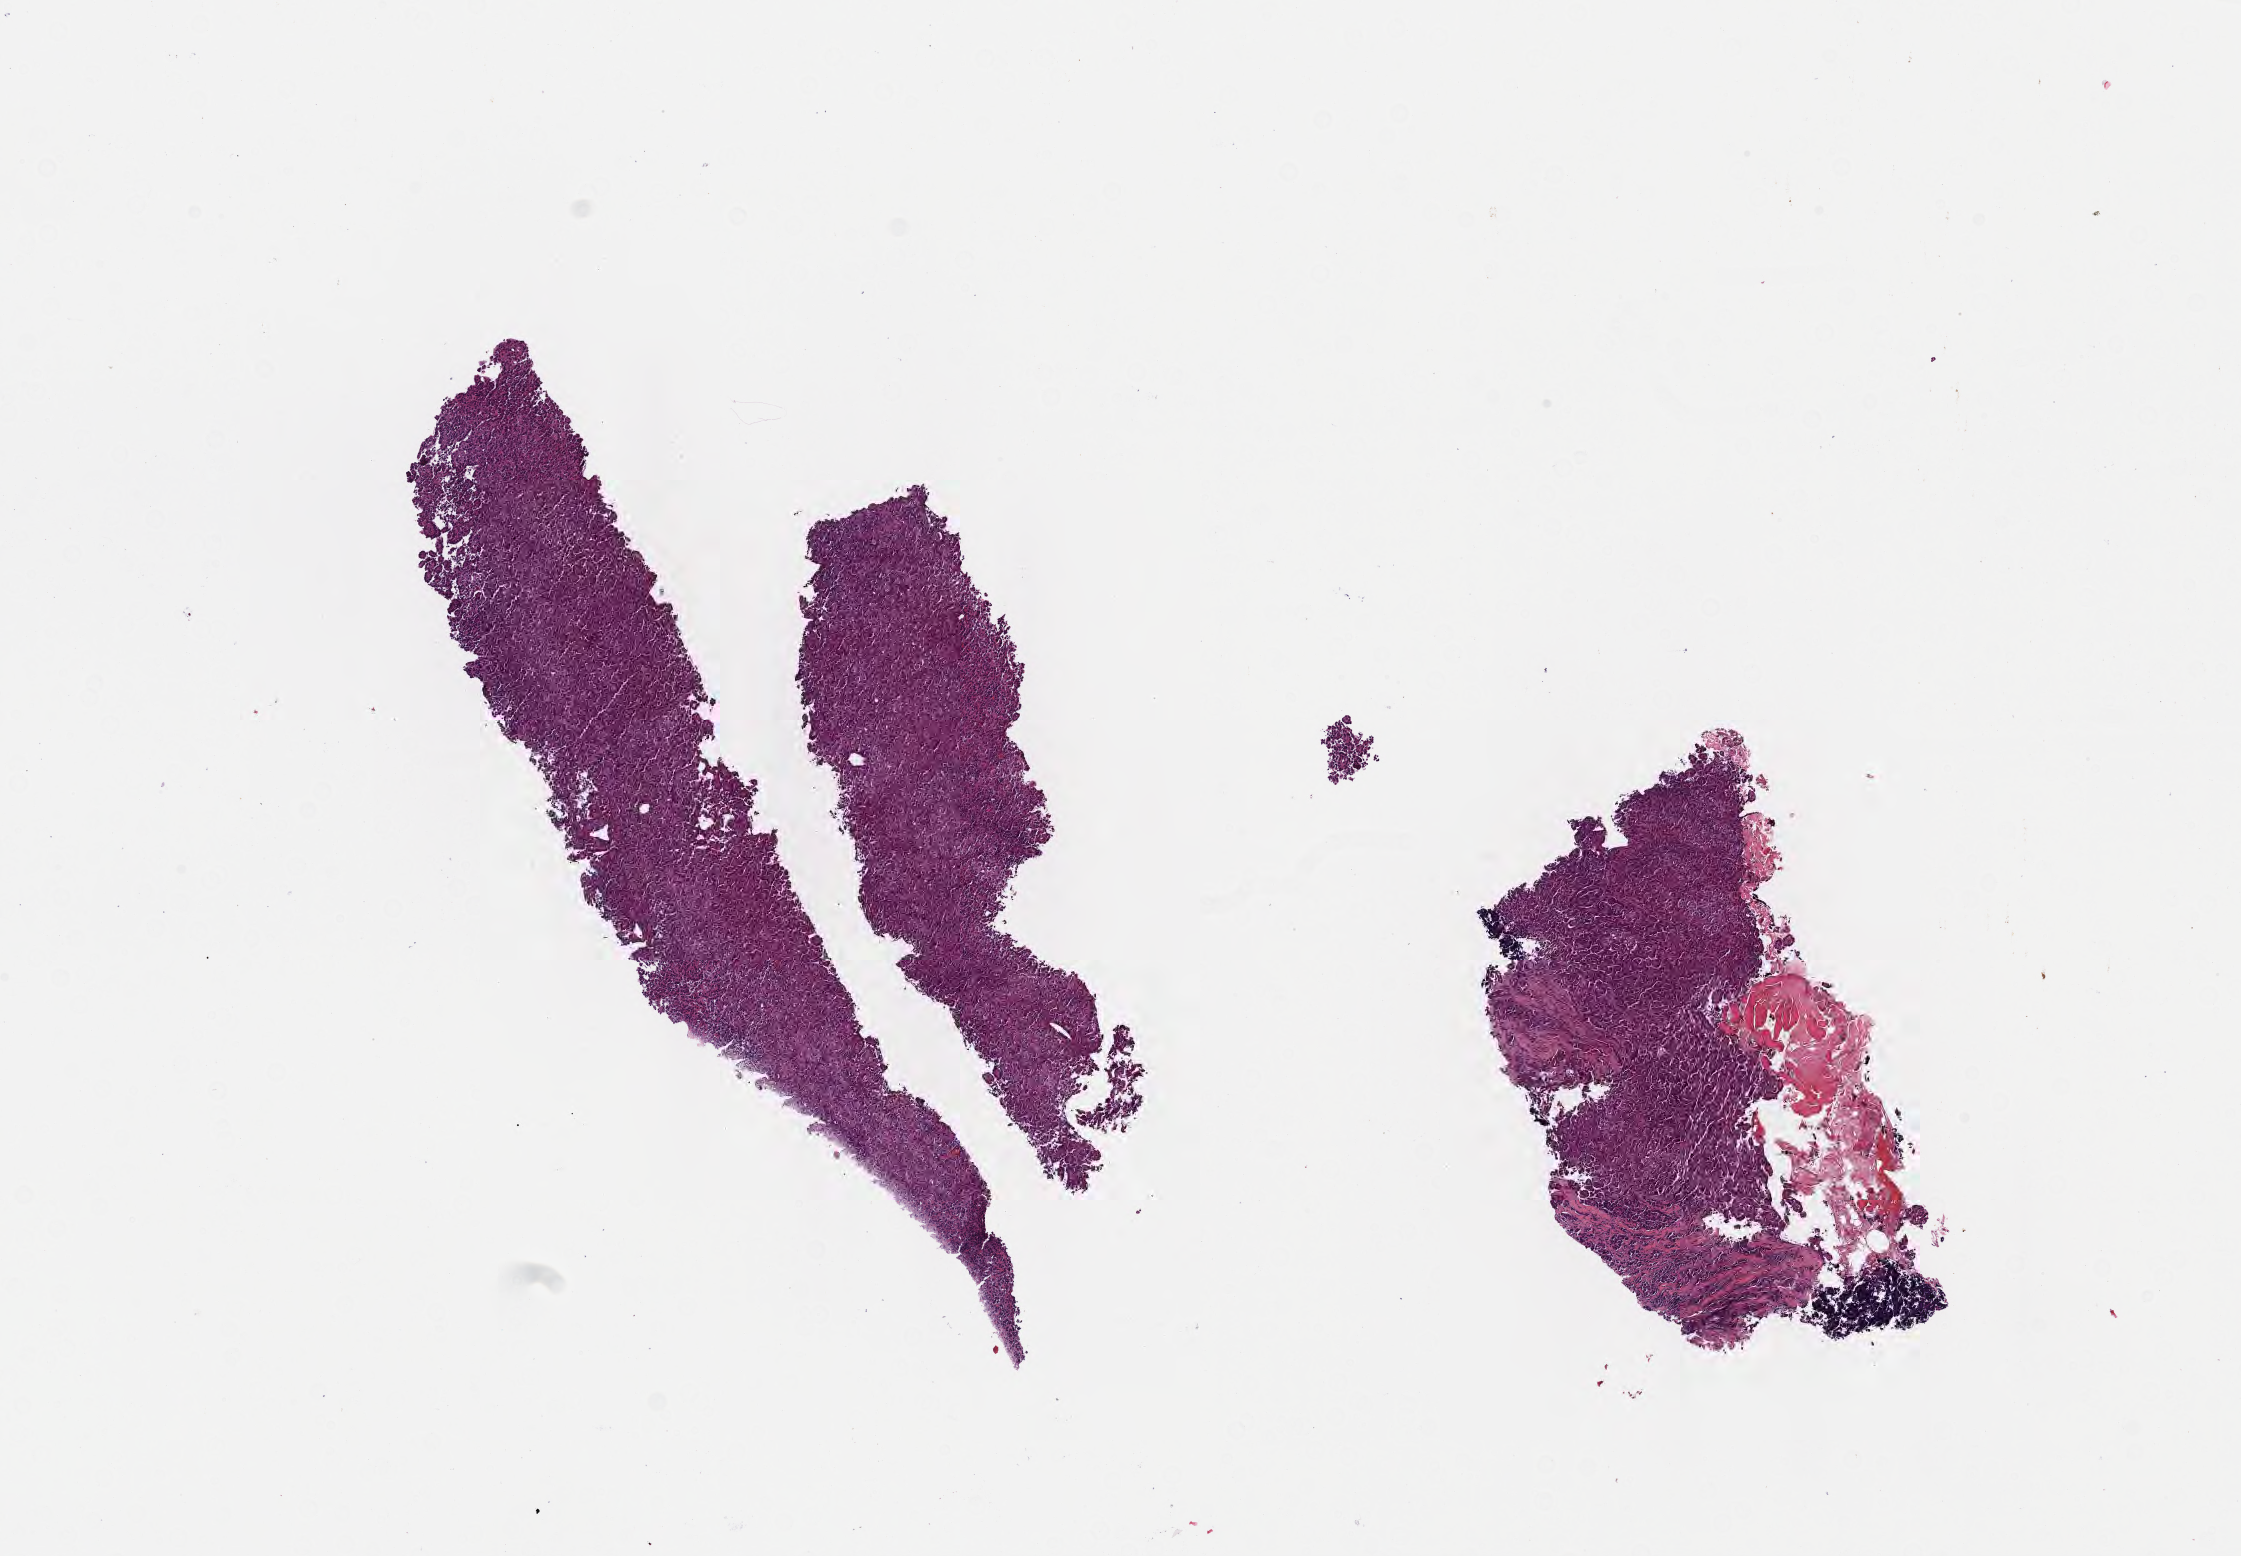
Whole-slide image, H&E stain — whole scanned area (about 9.1 x 6.3 mm) shown as a low-resolution overview, specimen: tumor tissue, site: lung. Patient female; 65 years old.
Histologic diagnosis: Non-small cell carcinoma.